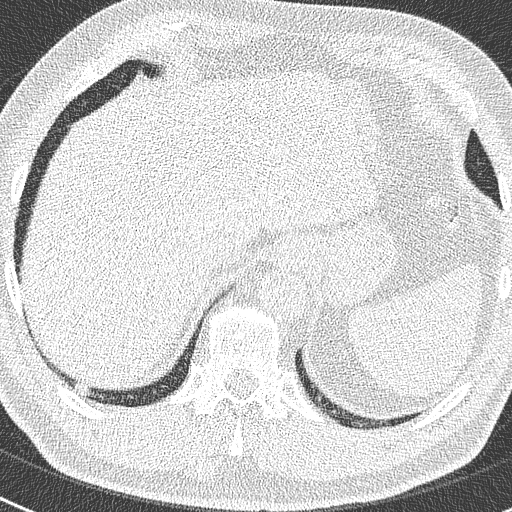
Chest CT (low-dose screening protocol), one axial image. Second screening round (one year after baseline). Lung window (W 1500 / L -600 HU). 2 mm slice thickness. Lung (sharp) reconstruction kernel (B50f). Slice 238 of 299 in the series. 512 × 512 image matrix, field of view 300 × 300 mm. Male, age 63 years at enrolment. Former smoker at enrolment.
Expert reader's lesion annotation, bounding box (x1, y1, x2, y2) in pixels: (66, 377, 98, 404). Screening reader's record for this exam: no non-calcified nodule ≥4 mm recorded. Official screen result: negative screen, no significant abnormalities. Participant outcome: lung cancer diagnosed 262 days after this screen — adenocarcinoma, NOS, right lower lobe, moderately differentiated (G2), stage IIIB (AJCC 6th edition), 17 mm at pathology.